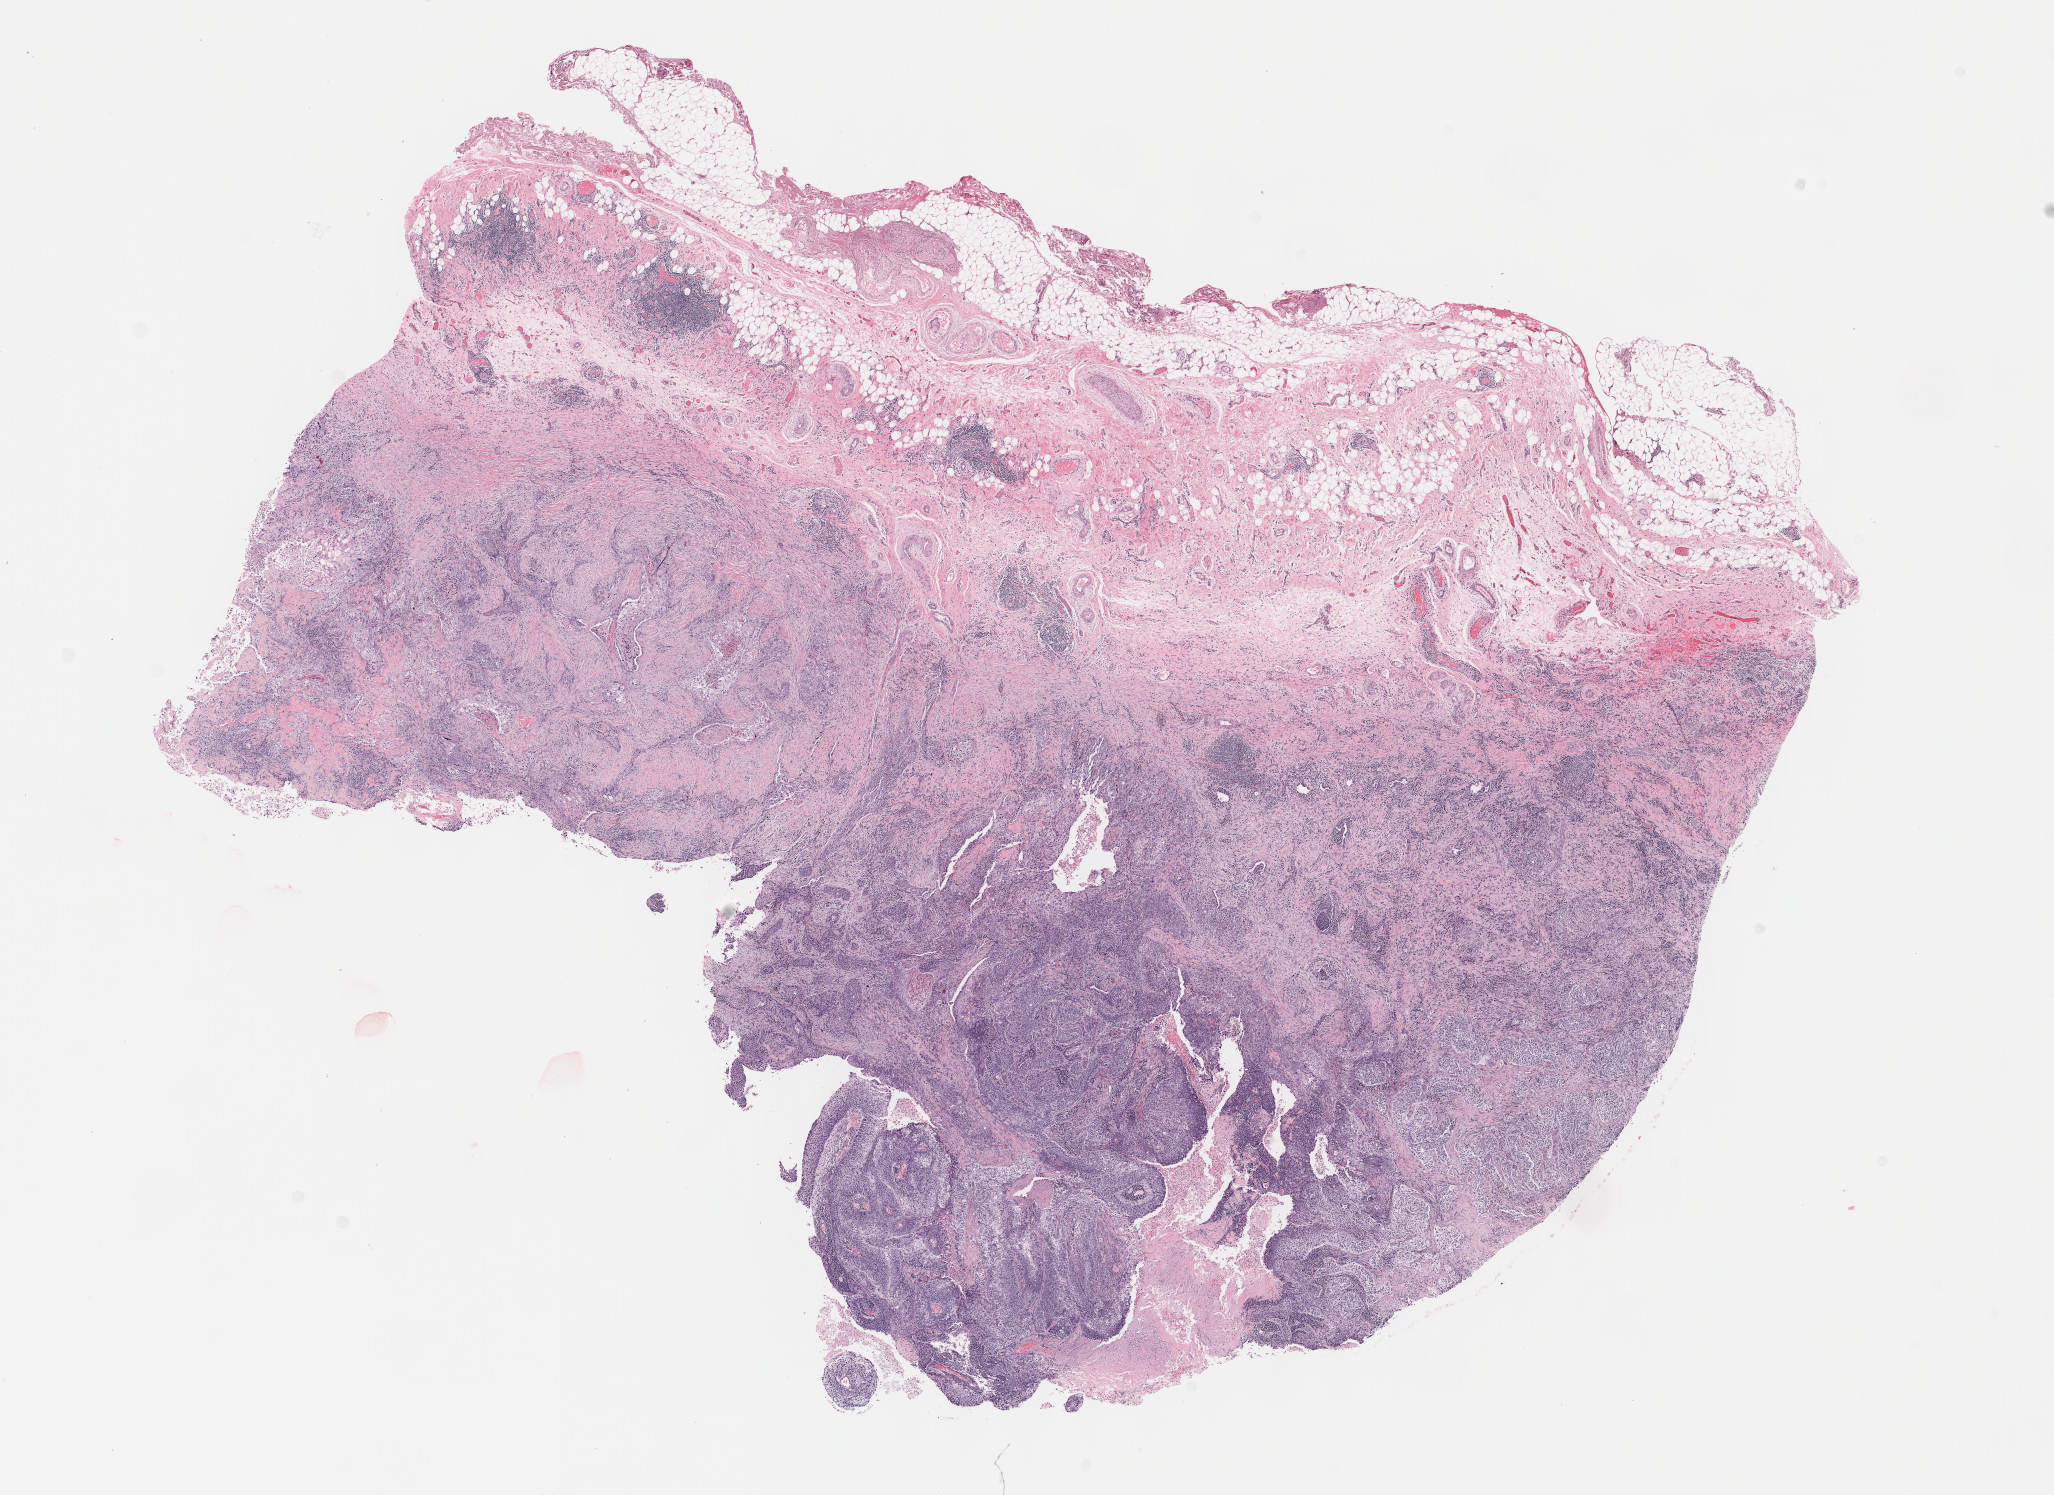
Digitized H&E-stained tissue section (whole slide) — low-resolution overview of the scanned area, about 16.6 x 12.1 mm (slide scanned at 40x); FFPE section; sample: primary tumour, lung. Male, age 64 years at initial diagnosis.
• laterality: right
• TNM: T2 N0 M0
• AJCC pathologic stage: IB
• histologic diagnosis: Squamous cell carcinoma, NOS (upper lobe, lung)